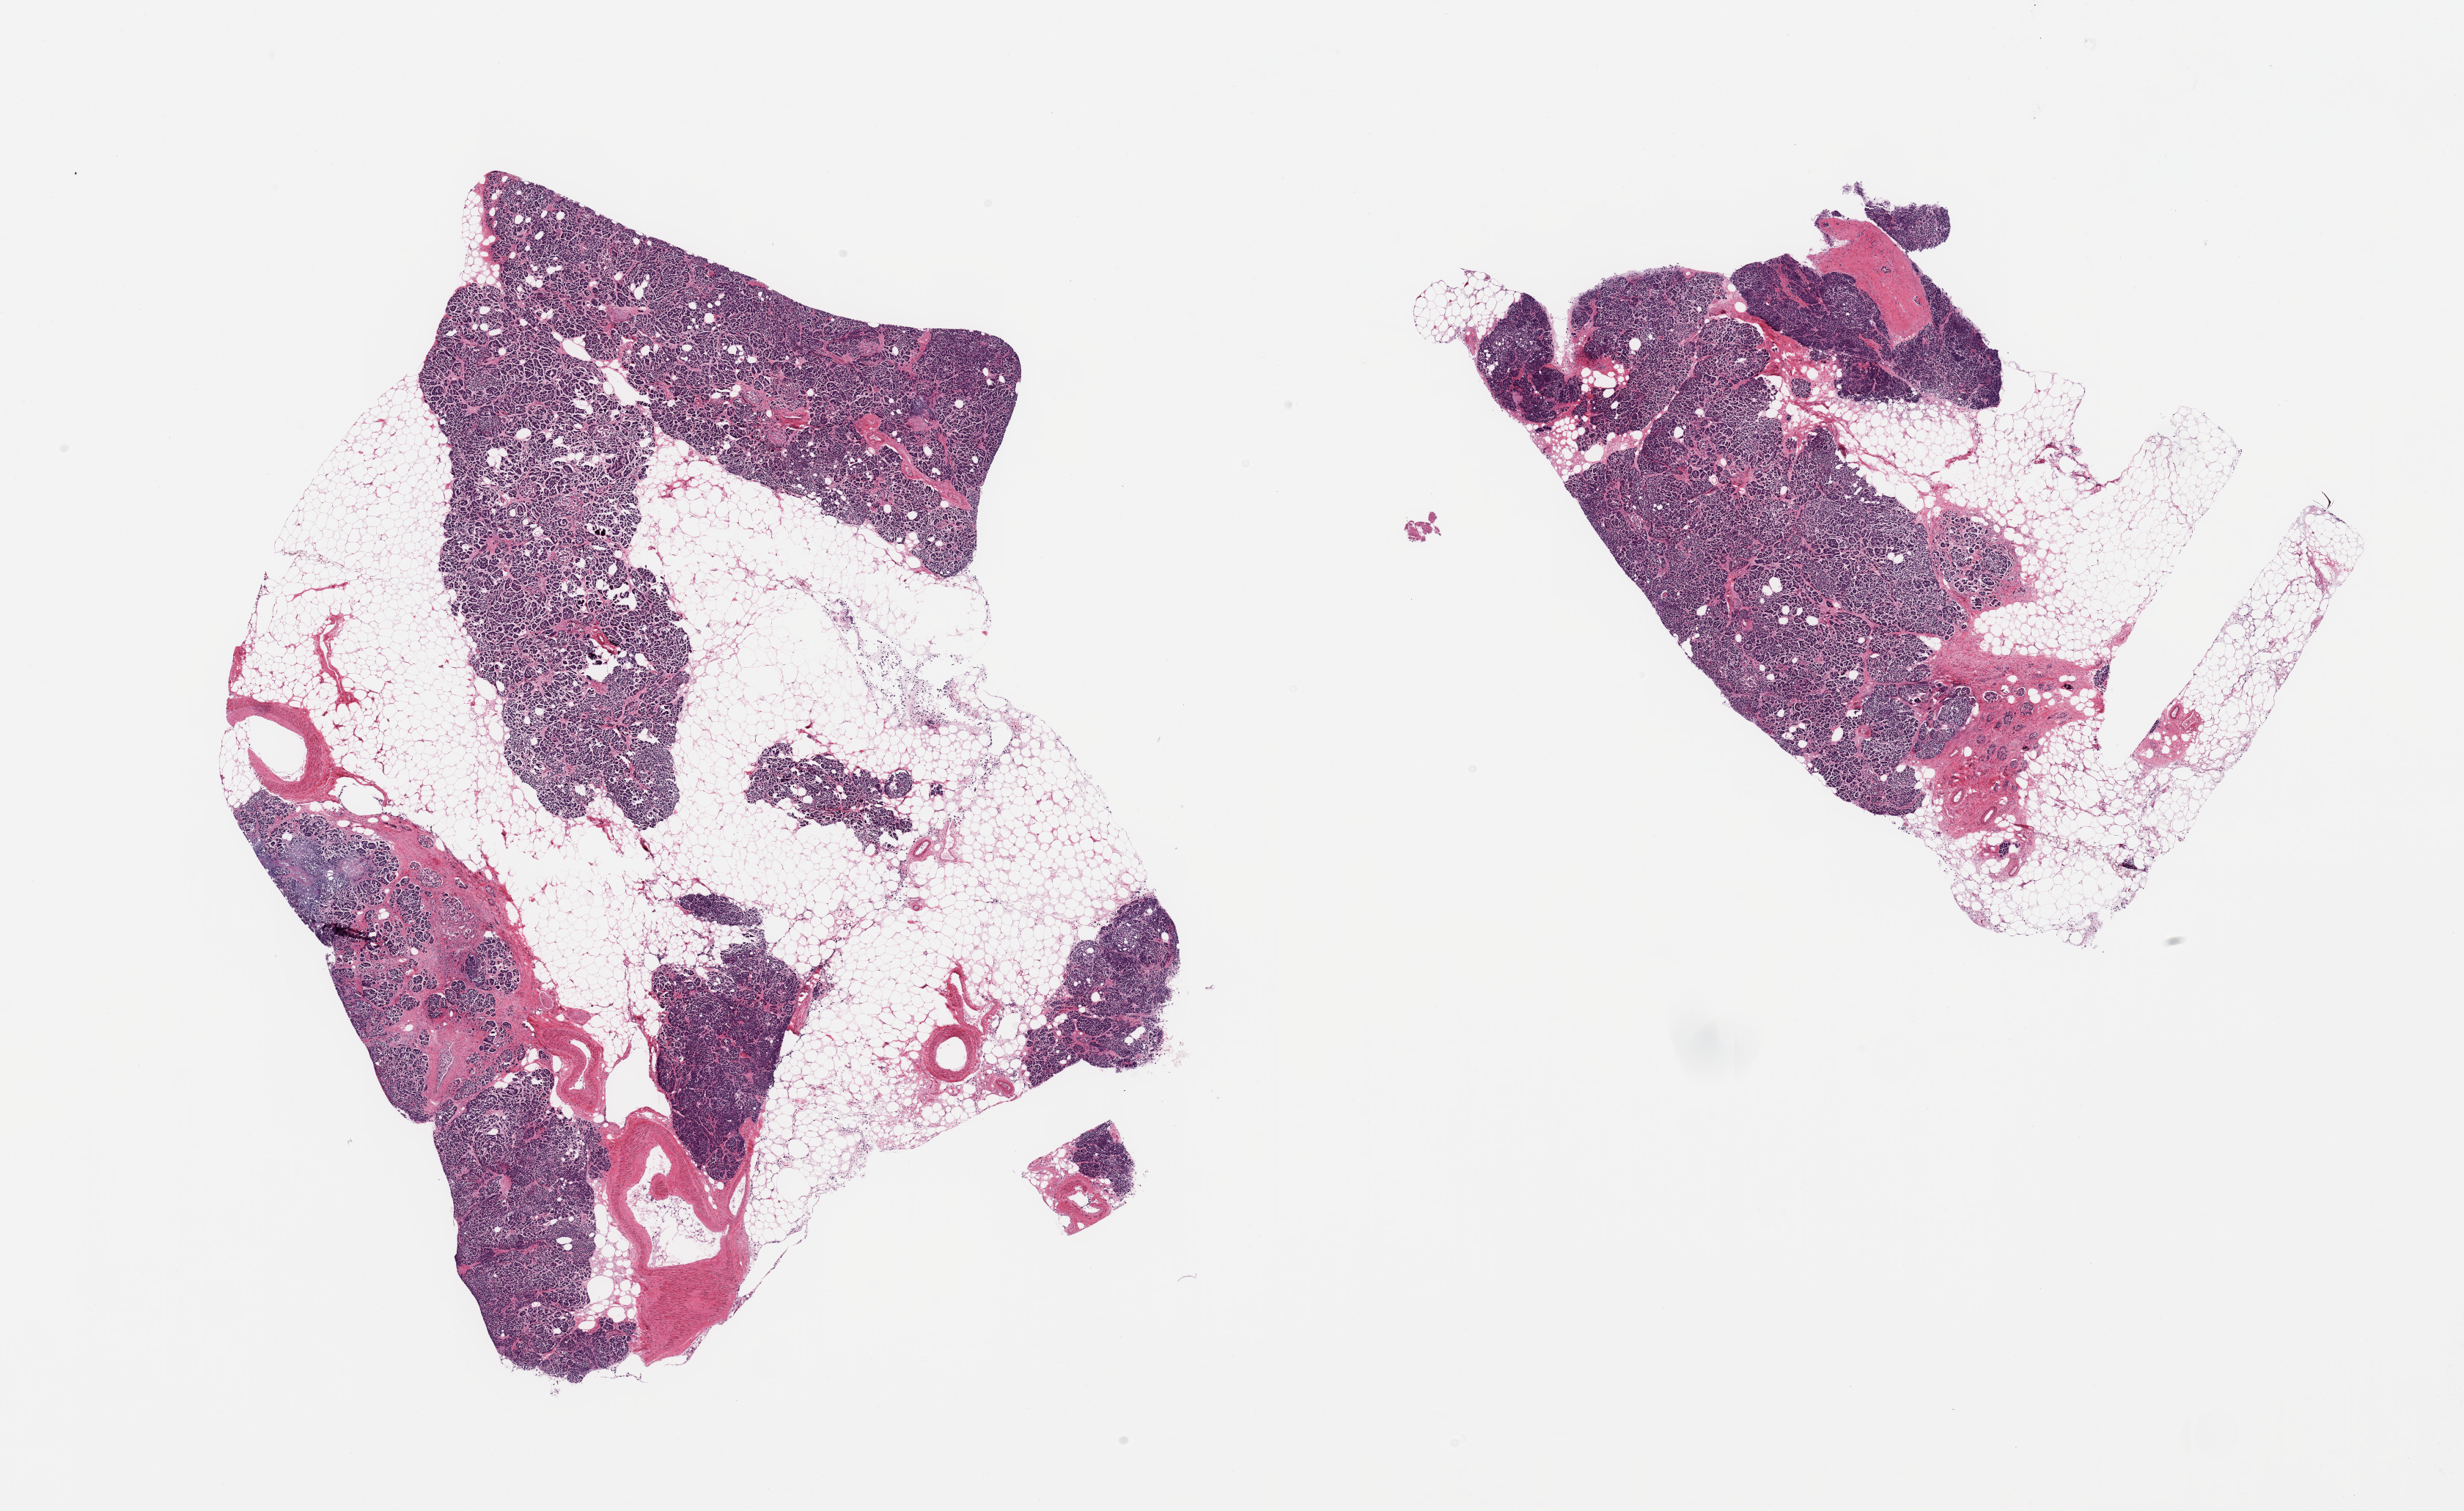
Whole-slide image, hematoxylin and eosin (H&E) stain, brightfield — whole scanned area (about 26.6 x 16.3 mm) shown as a low-resolution overview; PAXgene-fixed paraffin-embedded (PFPE) section; target tissue: pancreas; tissue donor sample.
* pathologist's review note for this sample: 2 pieces; 50% internal fat; partially fibrotic islets